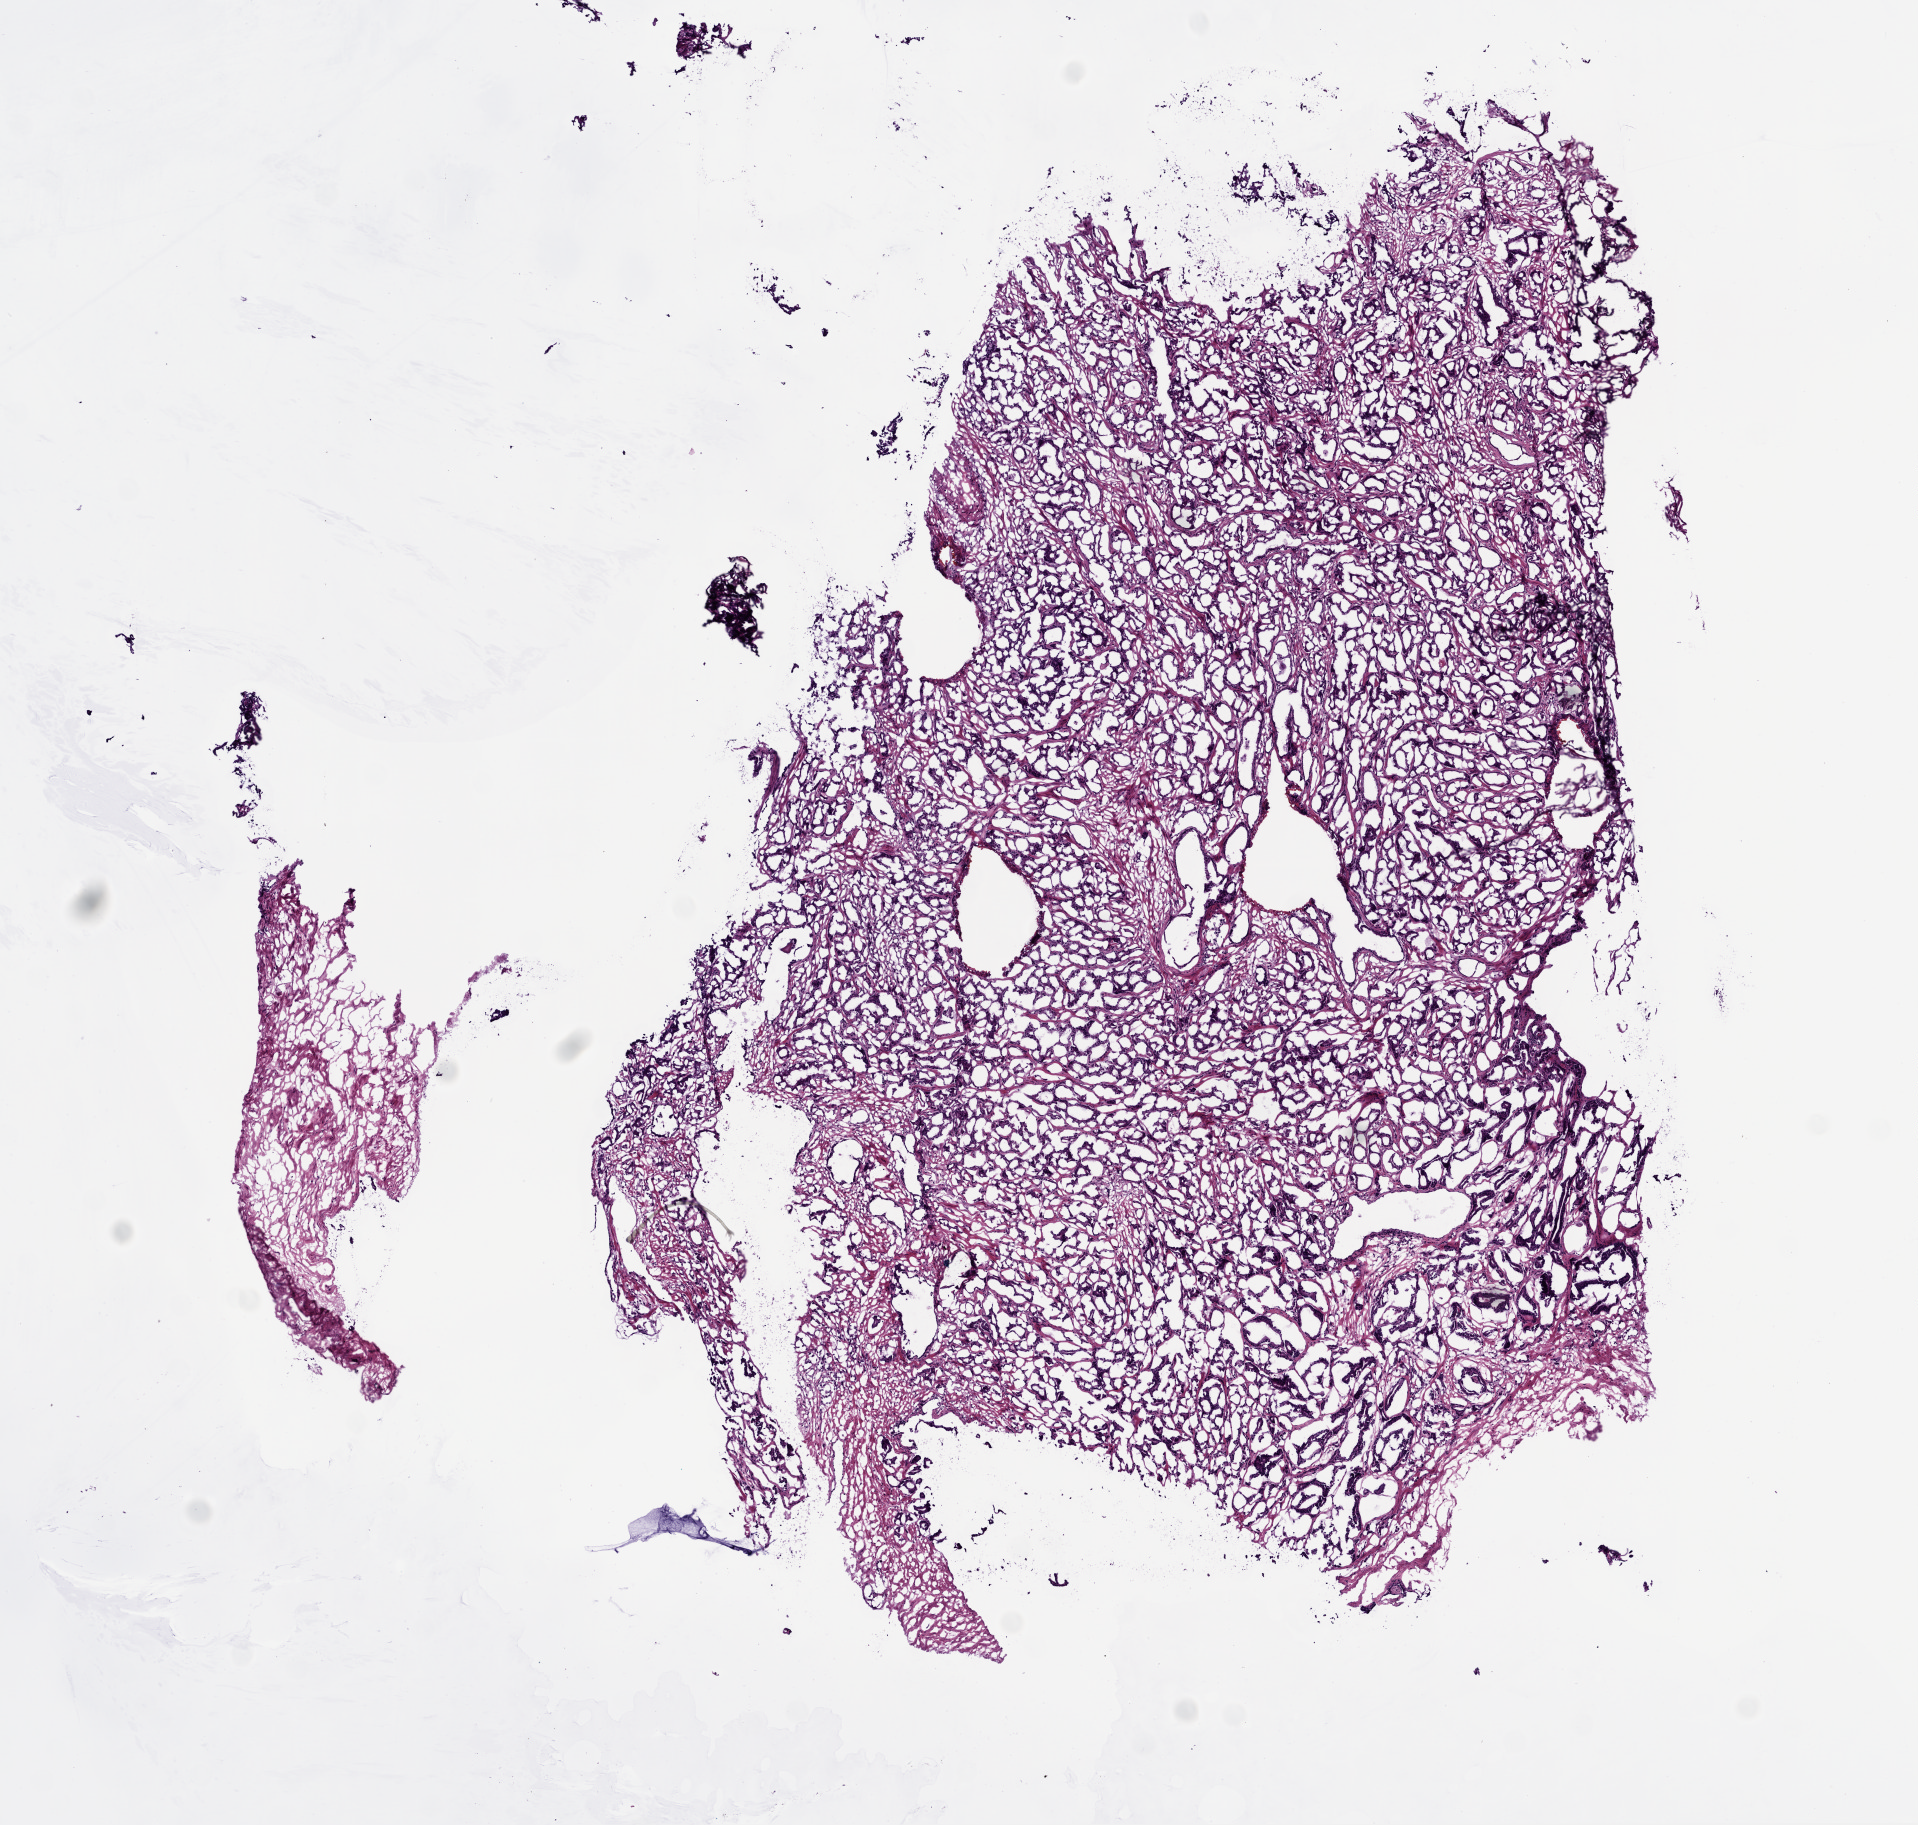
Hematoxylin and eosin (H&E) stained whole-slide image — whole scanned area (about 7.7 x 7.4 mm, from a 20x scan) shown as a low-resolution overview; frozen section; prostate, primary tumour sample. Male, age 64 years at initial diagnosis. Gleason score: 7 (4+3). Pathologist review of this section (percent, as recorded): tumour nuclei 70%, necrosis 0%.
Diagnosis: Acinar cell carcinoma.